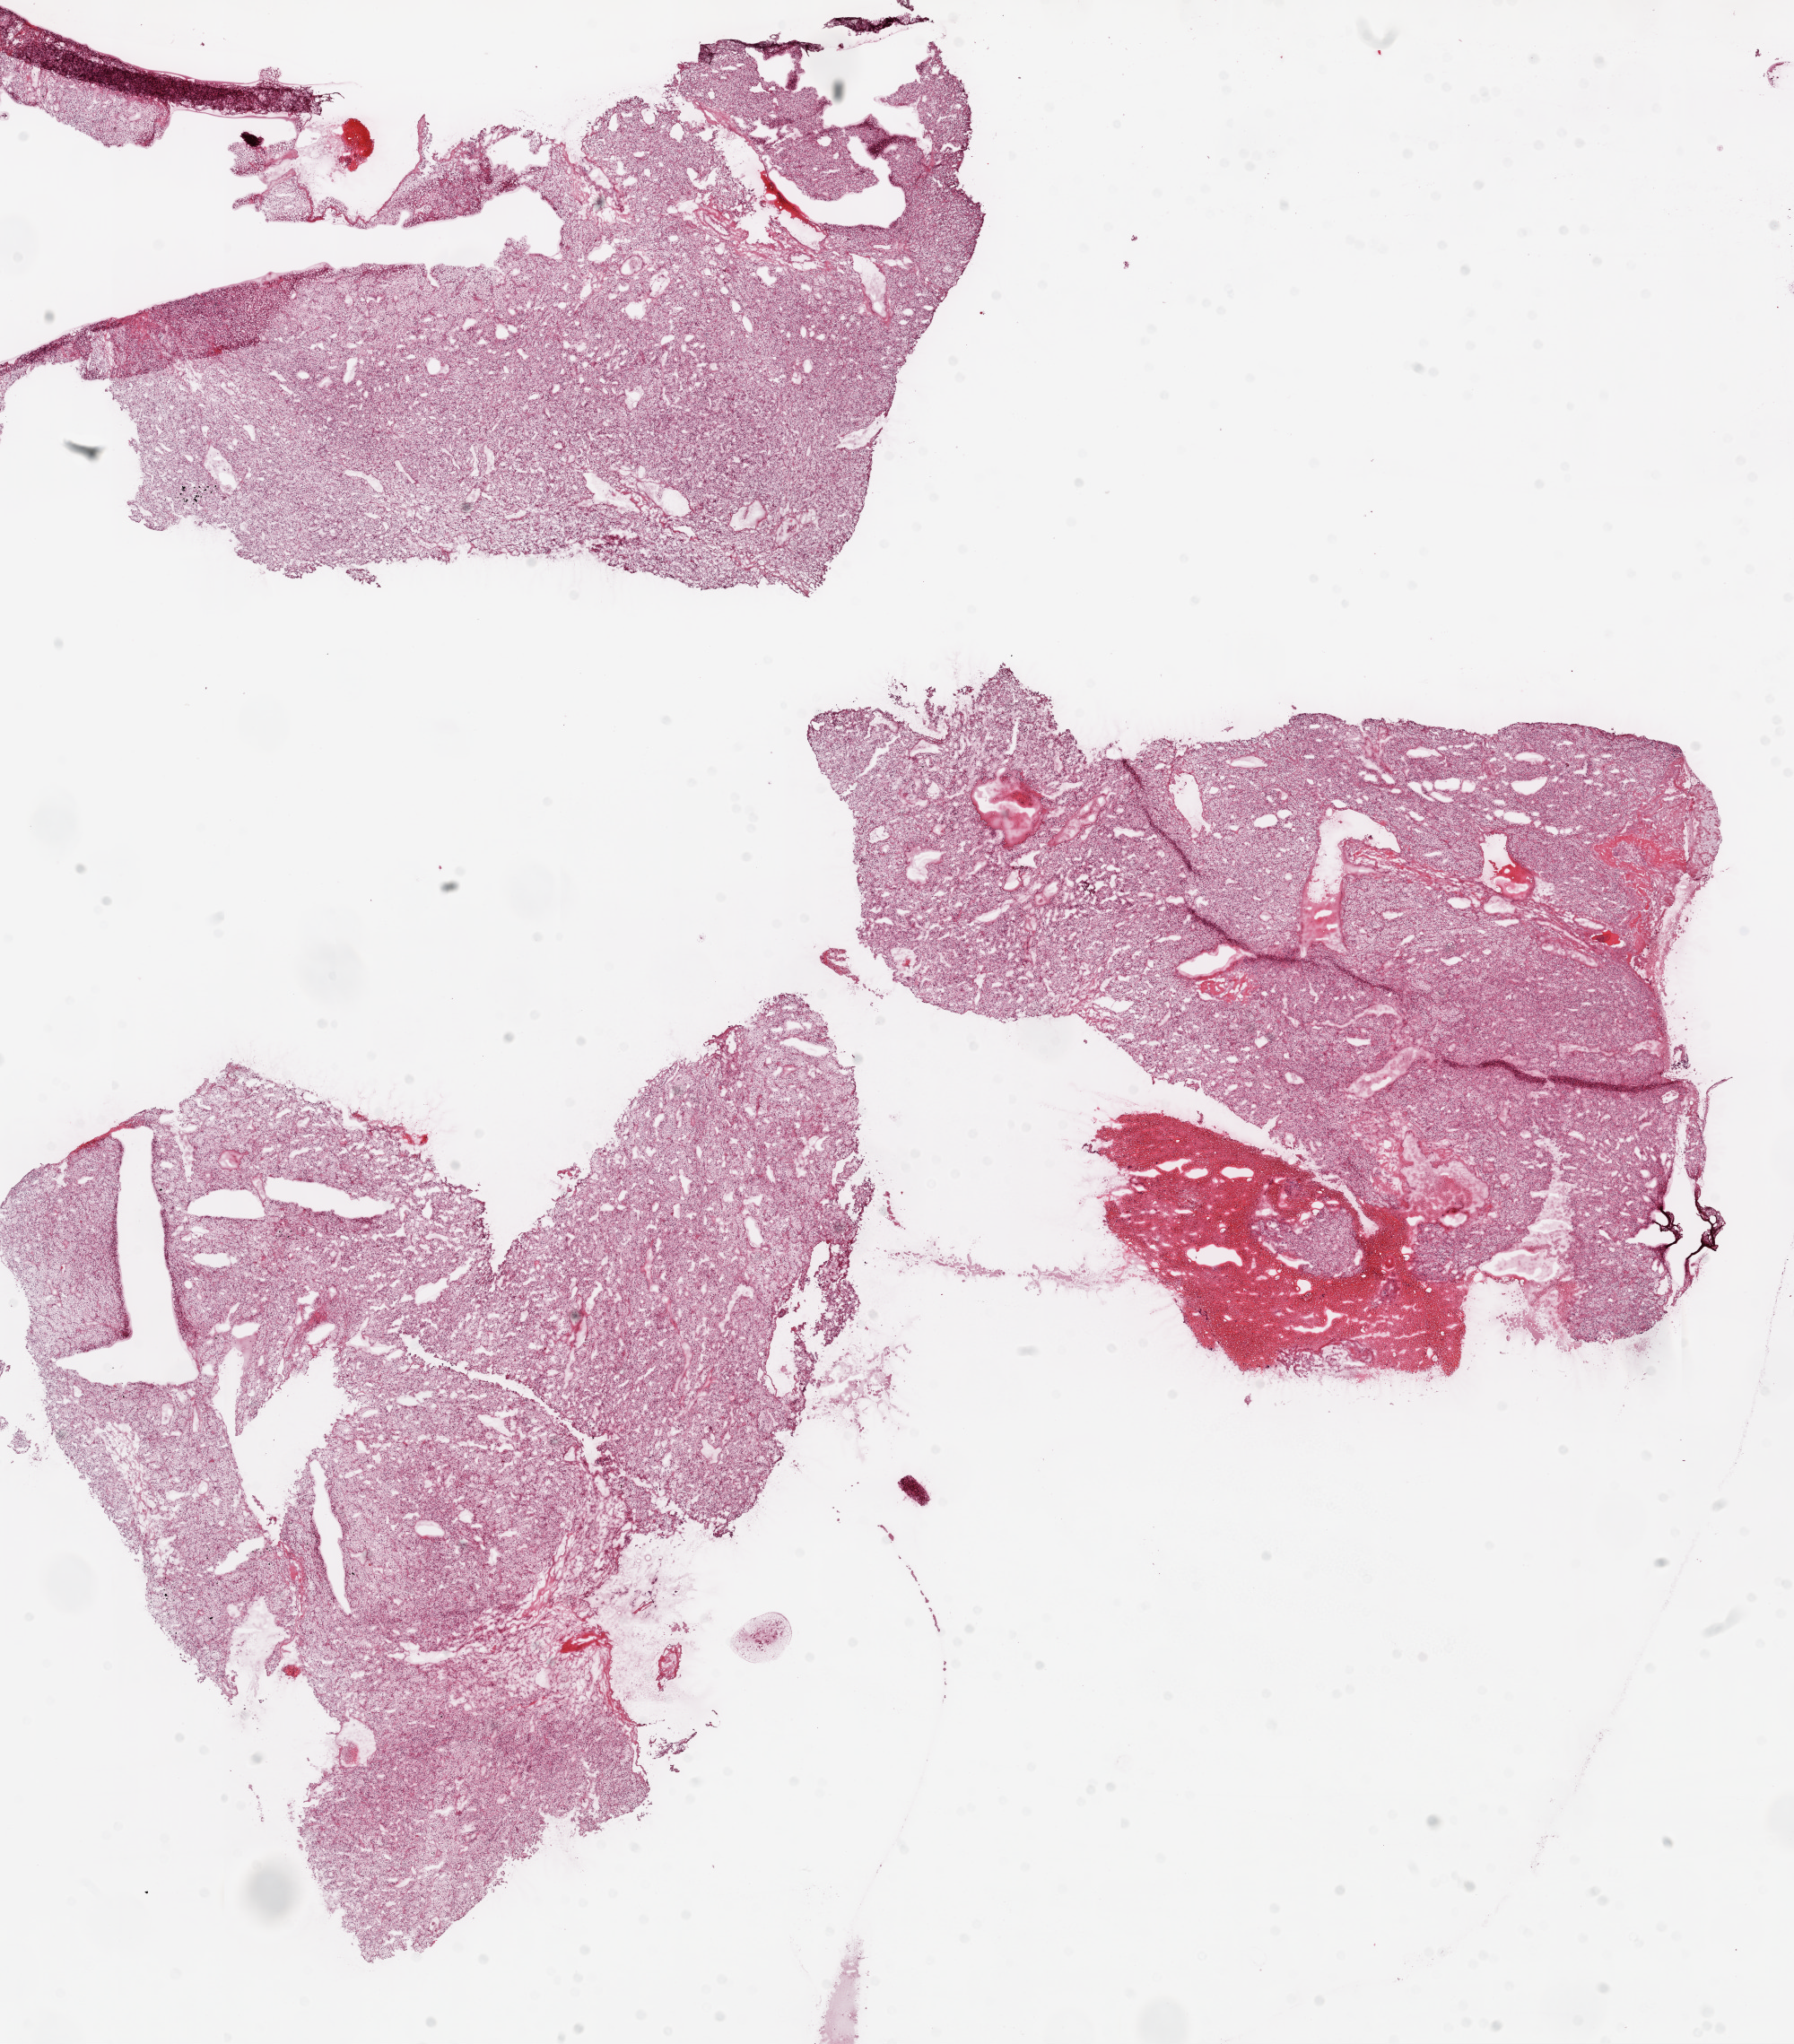
Whole-slide histology image, Hematoxylin and eosin (H&E) stained — whole scanned area (about 16.0 x 18.3 mm) shown as a low-resolution overview; frozen section from the top of the tissue portion; kidney, primary tumour sample. Male patient; age at initial diagnosis 45 years. Histologic grade: G2 (moderately differentiated). Slide review estimates, as recorded: tumour cells 90%, tumour nuclei 85%, normal cells 0%, stromal cells 10%, necrosis 0%.
• lymph nodes positive (case pathology): 0 of 10 examined
• laterality: left
• TNM: T2 N0 M0
• histologic diagnosis: Clear cell adenocarcinoma, NOS
• AJCC pathologic stage: II